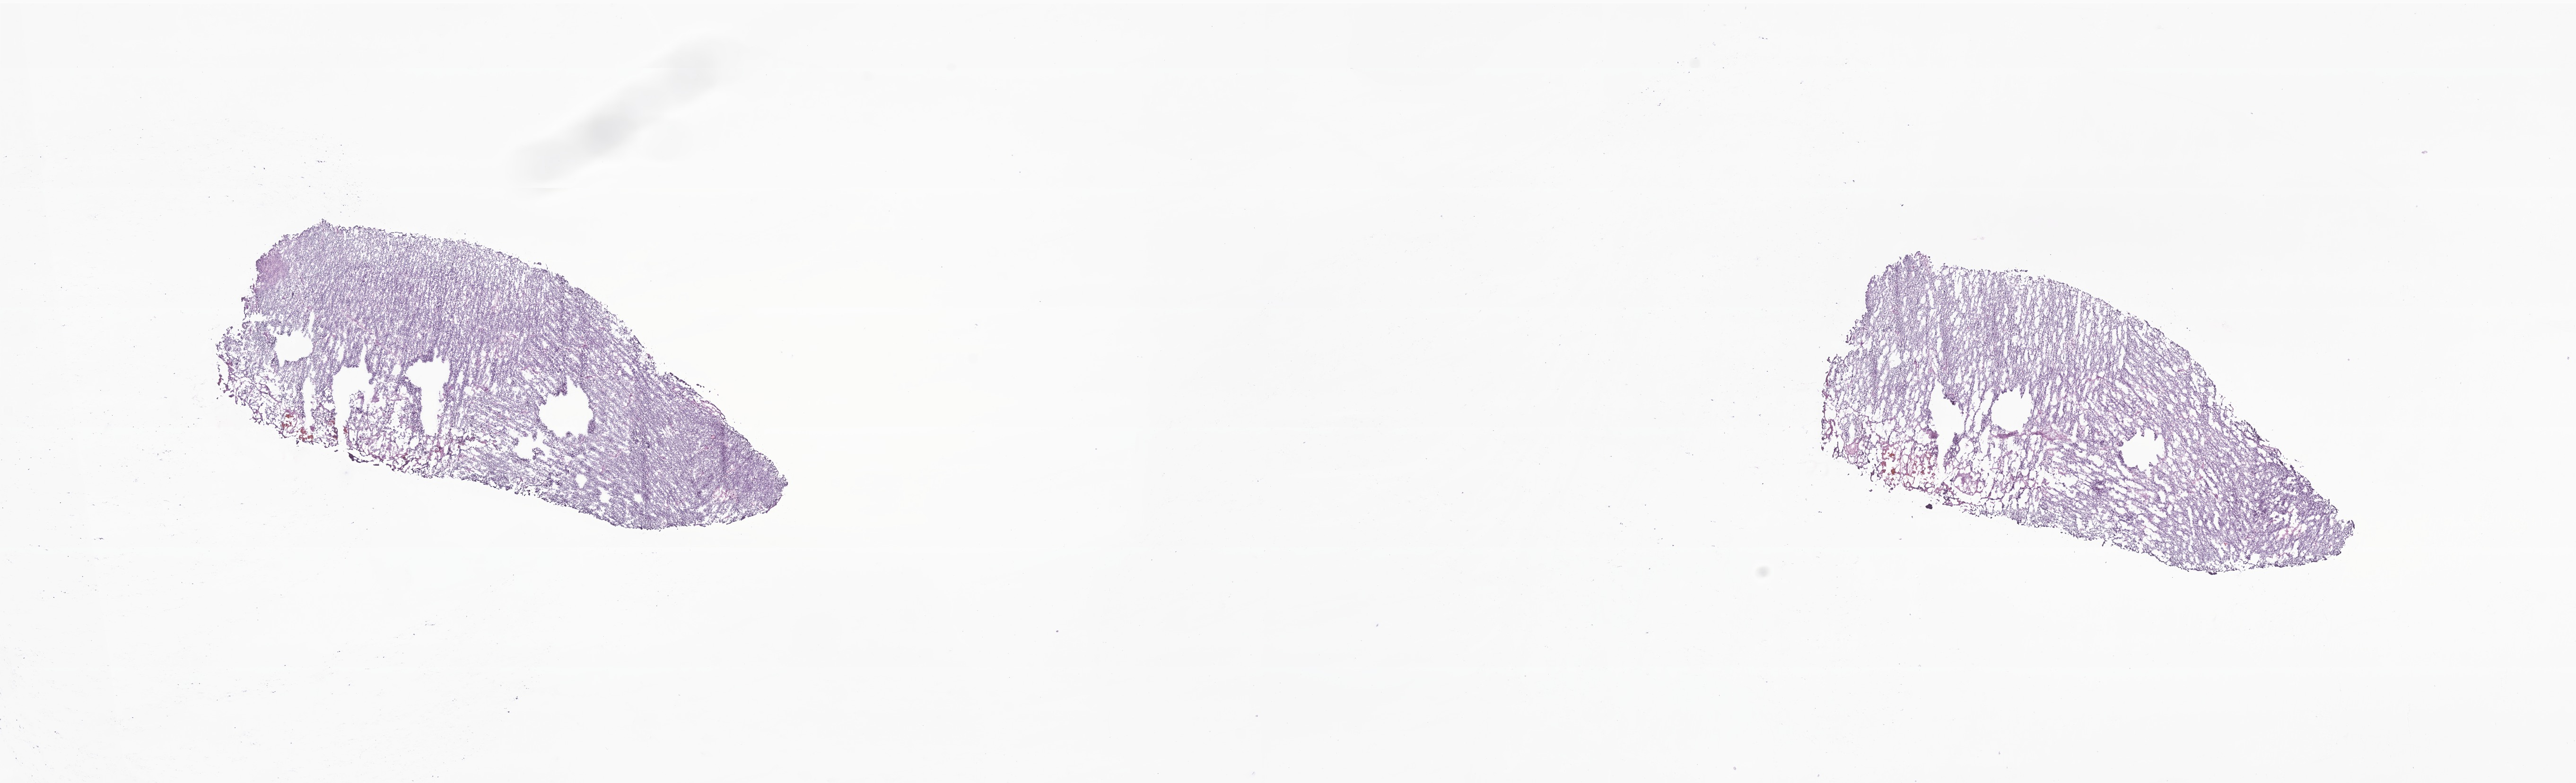
Digitized H&E-stained section of tumor tissue from the cerebellum, a low-resolution overview of the entire scanned area, about 23.0 x 7.0 mm, frozen section (OCT-embedded). Female patient, age 88 months (7 years 4 months).
Diagnosis: Medulloblastoma, NOS.